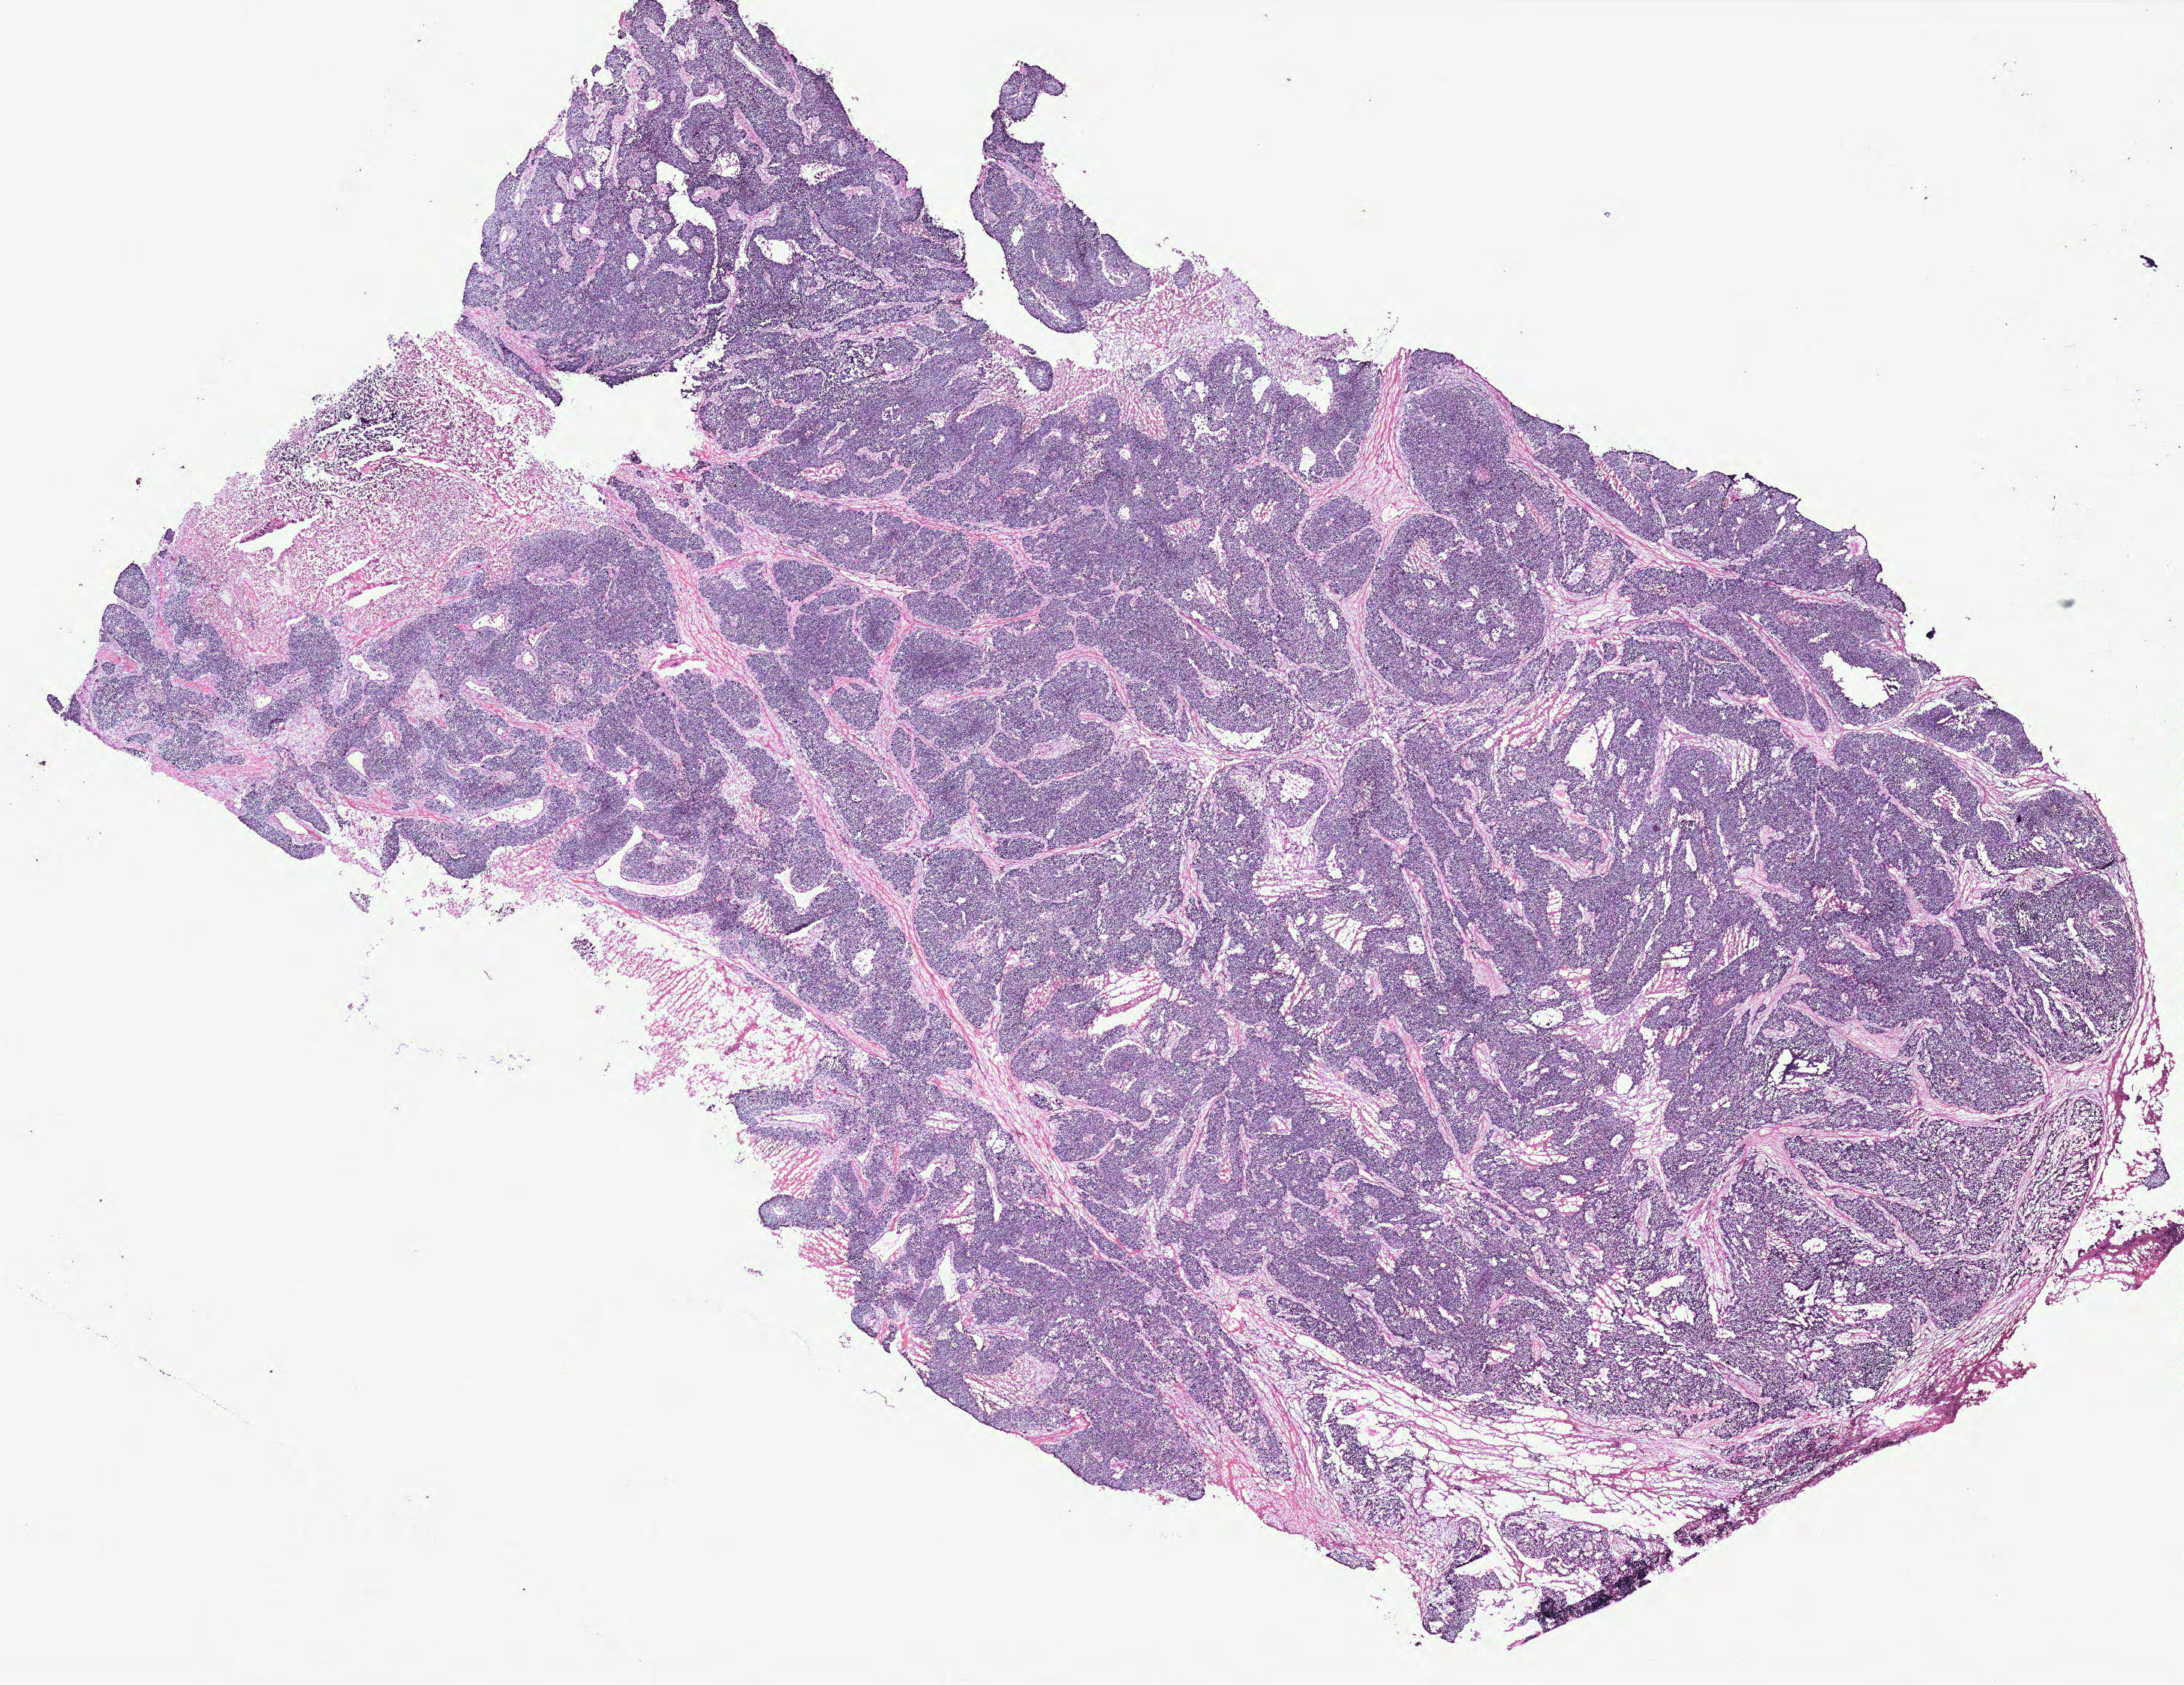
Digitized H&E tissue section (whole slide) — whole scanned area (about 23.3 x 18.0 mm, acquisition: 40x scan) shown as a low-resolution overview, breast, tissue type not recorded. Female, 51 y/o.
- patient diagnosis: Infiltrating duct carcinoma, NOS